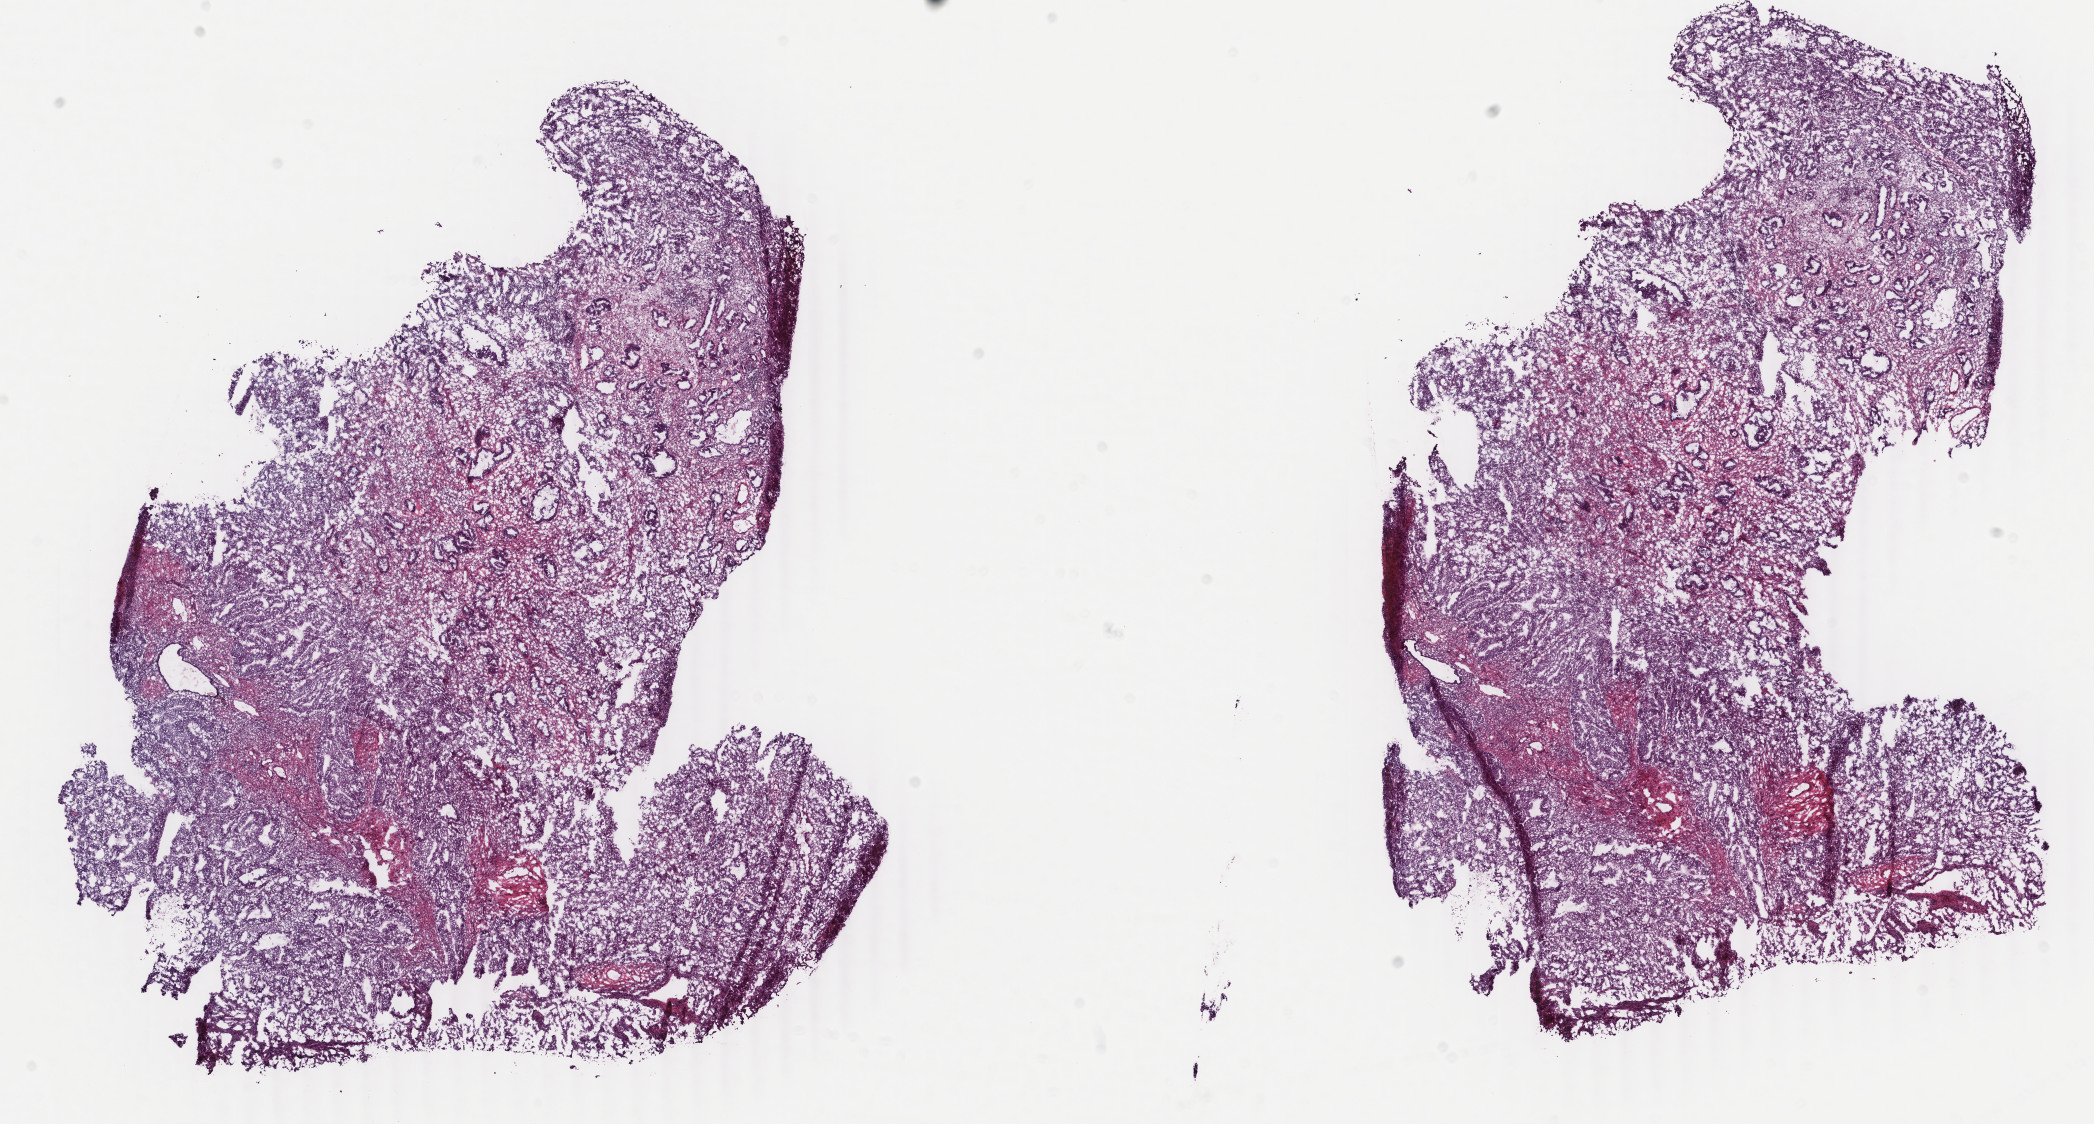
Whole-slide histology image, Hematoxylin and eosin (H&E) stained, low-resolution overview of the scanned area, about 16.7 x 8.9 mm (acquisition: 40x scan), frozen section, primary tumour sample from the uterus. Female, age 48 years at initial diagnosis. Histologic grade: G1 (well differentiated). Pathologist review of this section (percent, as recorded): tumour cells 30%, tumour nuclei 35%, normal cells 15%, stromal cells 47%, necrosis 2%. Infiltration values recorded for this section: lymphocyte infiltration 20%, monocyte infiltration 2%, neutrophil infiltration 1%.
FIGO stage: IB. Lymph nodes positive (case pathology): 0 of 26 examined. Diagnosis: Endometrioid adenocarcinoma, NOS (endometrium).